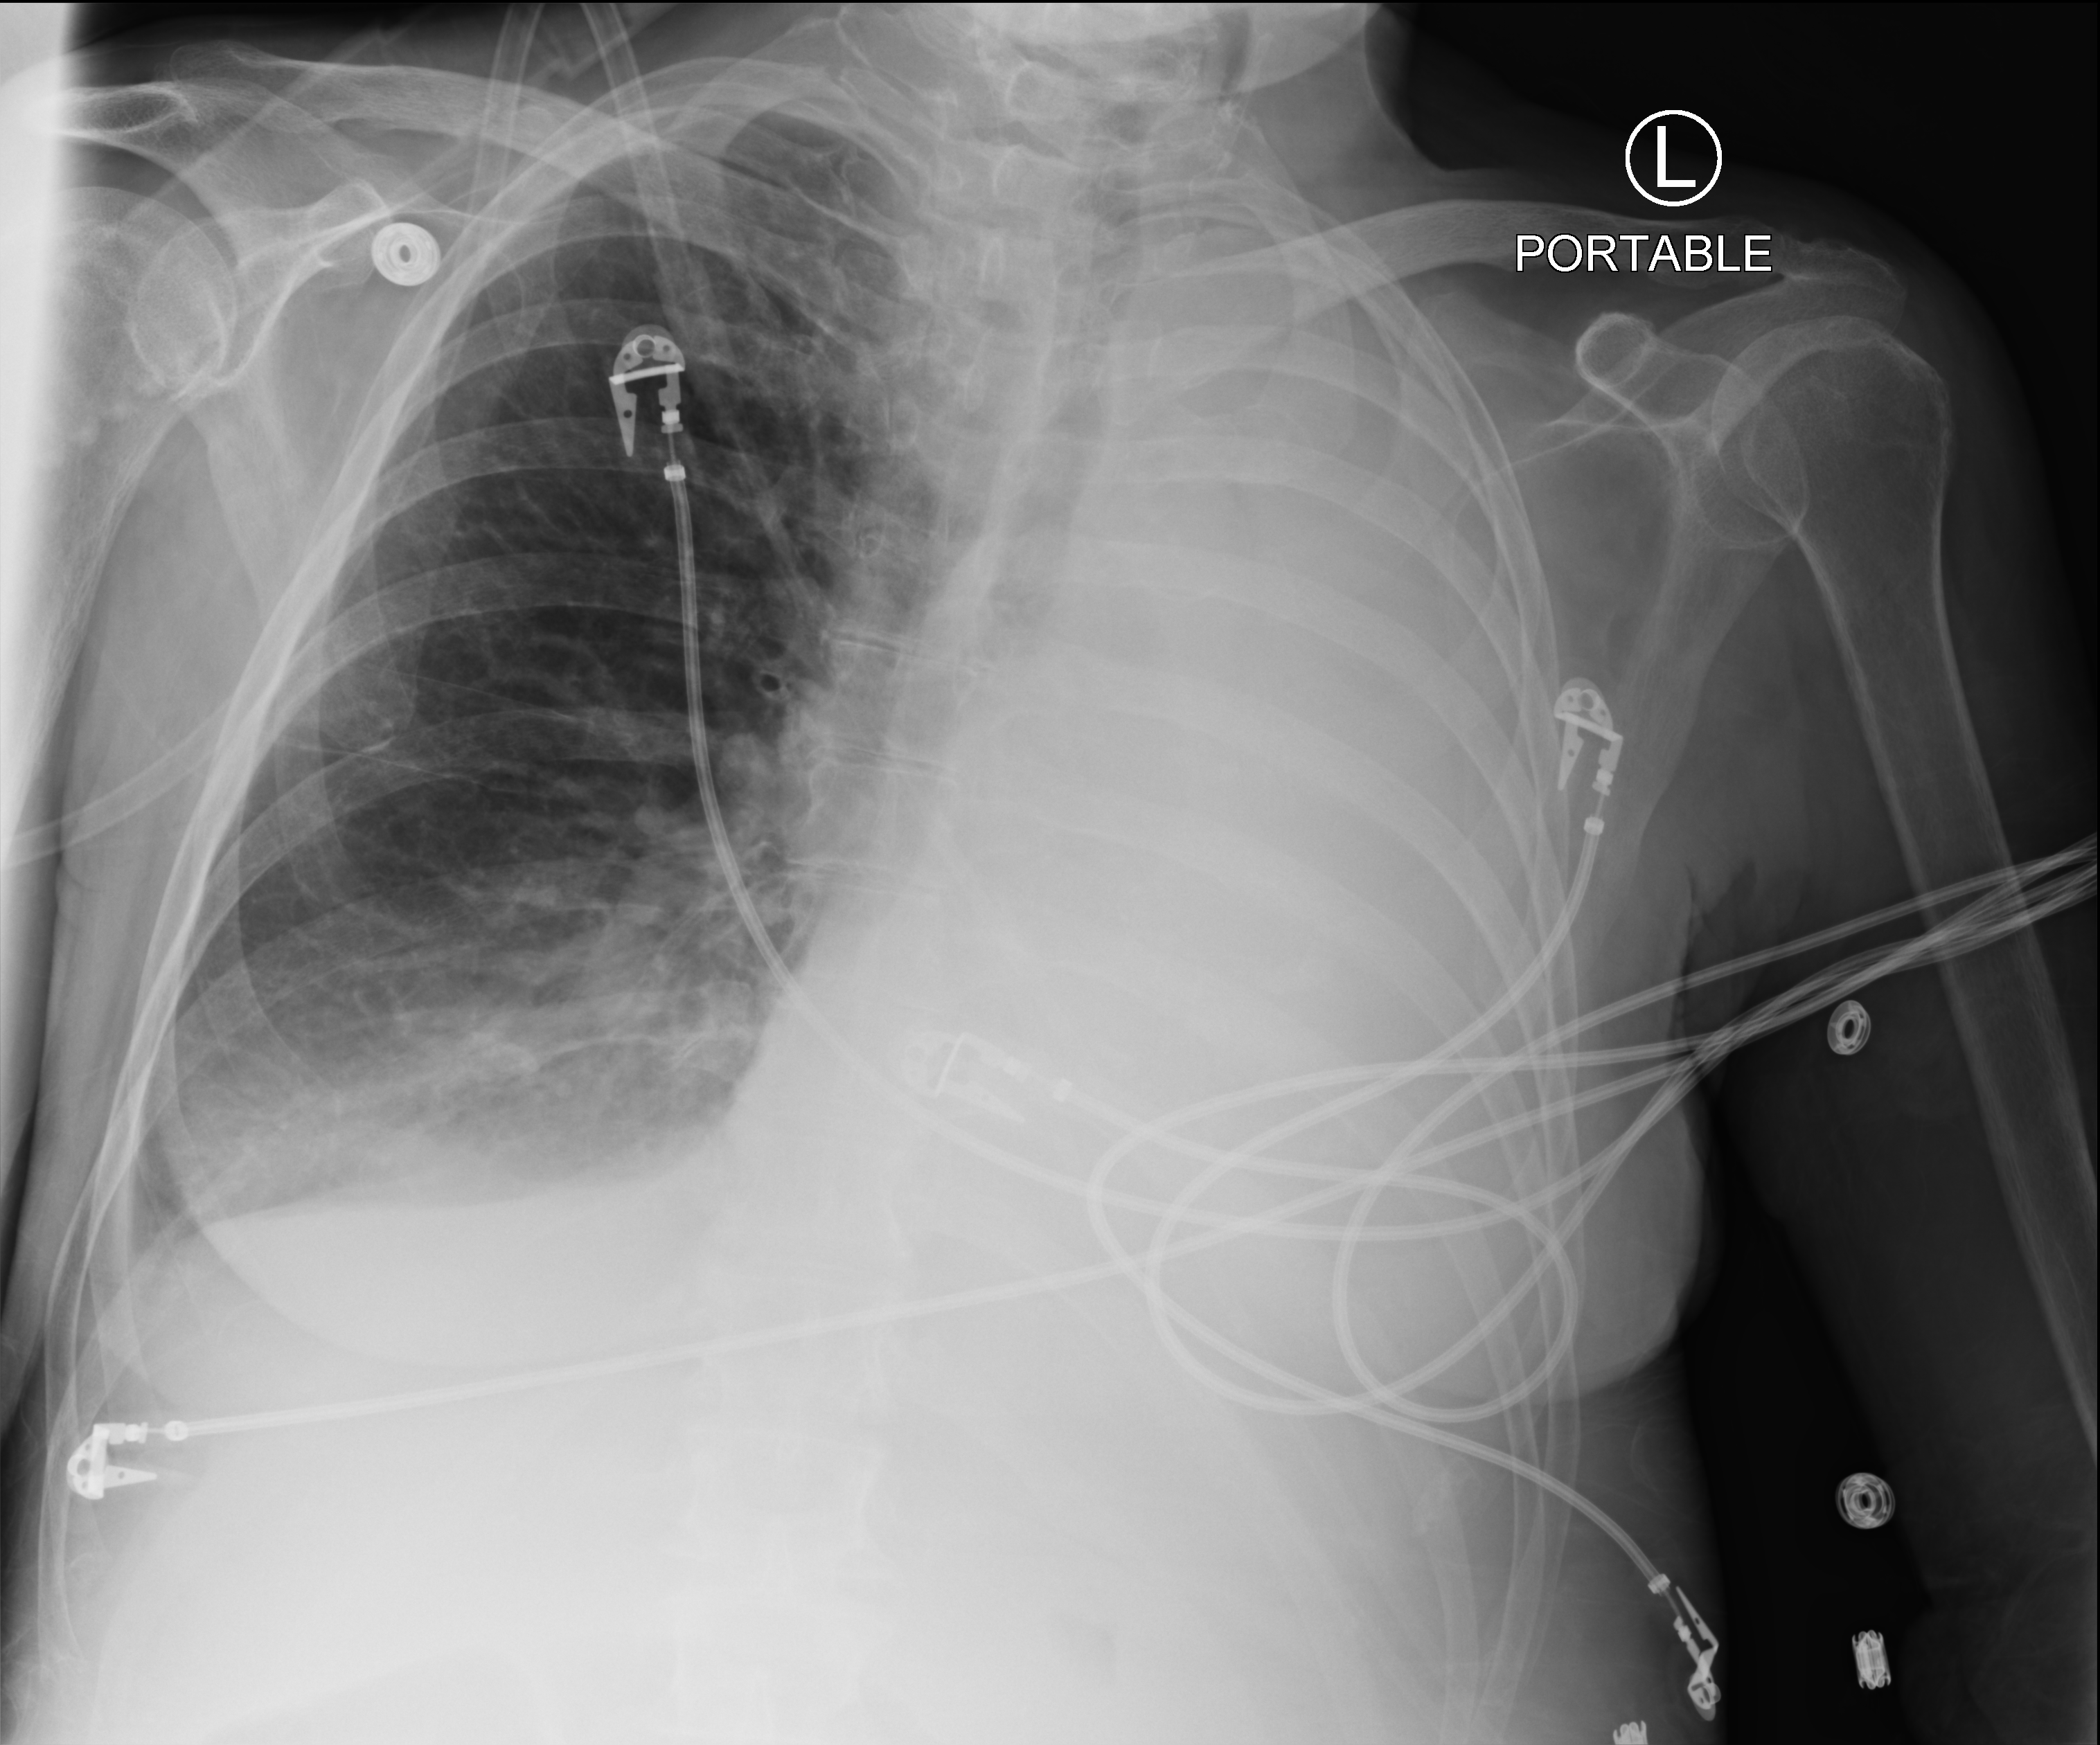
Chest X-ray (portable), anteroposterior (AP) projection. Female patient hospitalised with COVID-19, age 60–74 years.
Admission-level facts for this patient (not findings on this image; timing relative to this image not recorded):
- mechanically ventilated during this hospital stay: yes
- admitted to intensive care during this hospital stay: yes